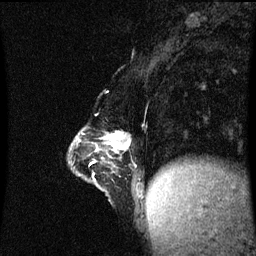
Breast MRI (dynamic contrast-enhanced), one sagittal slice; position 20 of 60 along the scan axis; dynamic contrast-enhanced series, image 2 of 3 at this slice position (ordered by acquisition); 1.5 T; TE 4.2 ms, TR 8.9 ms; 2 mm slice thickness; 256 × 256 image matrix. Patient: female, 47 years. Case-level facts recorded for this patient, not image findings: setting: breast cancer imaged before/during neoadjuvant chemotherapy; receptor status: HR-positive, HER2-negative.
Structures marked on this image (semi-automatically segmented with operator editing):
- analysis volume of interest (the breast-tissue region the enhancement analysis was run in; not a lesion): bounding box (x1, y1, x2, y2) in pixels: (70, 126, 148, 191)
- tumour enhancement mask (voxels above the 70 % enhancement threshold inside the analysis volume of interest): (110, 134, 130, 151)